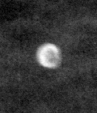
Cropped region of a digitized screen-film mammogram centred on a radiologist-marked abnormality, left breast, CC view, BI-RADS breast density category 1 (scale 1–4).
- Finding: calcifications, morphology lucent center; BI-RADS assessment category 2; benign; no additional work-up was recommended (benign without callback).